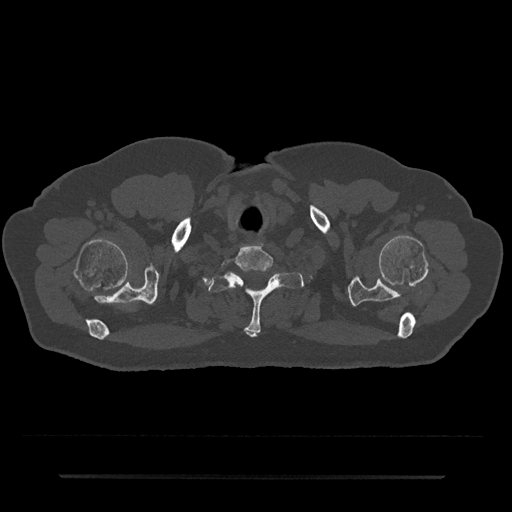
CT including the spine, one axial slice. Position 652 of 797 along the scan axis. Bone window (W 1800 / L 400 HU). 512 × 512 image matrix, field of view 437 × 437 mm. Patient: male, 69 years. Case-level facts recorded for this patient, not image findings: primary cancer: prostate.
Structures marked on this image (semi-automatically segmented with operator editing):
- T1 vertebra: box from (x=208, y=272) to (x=304, y=337) px